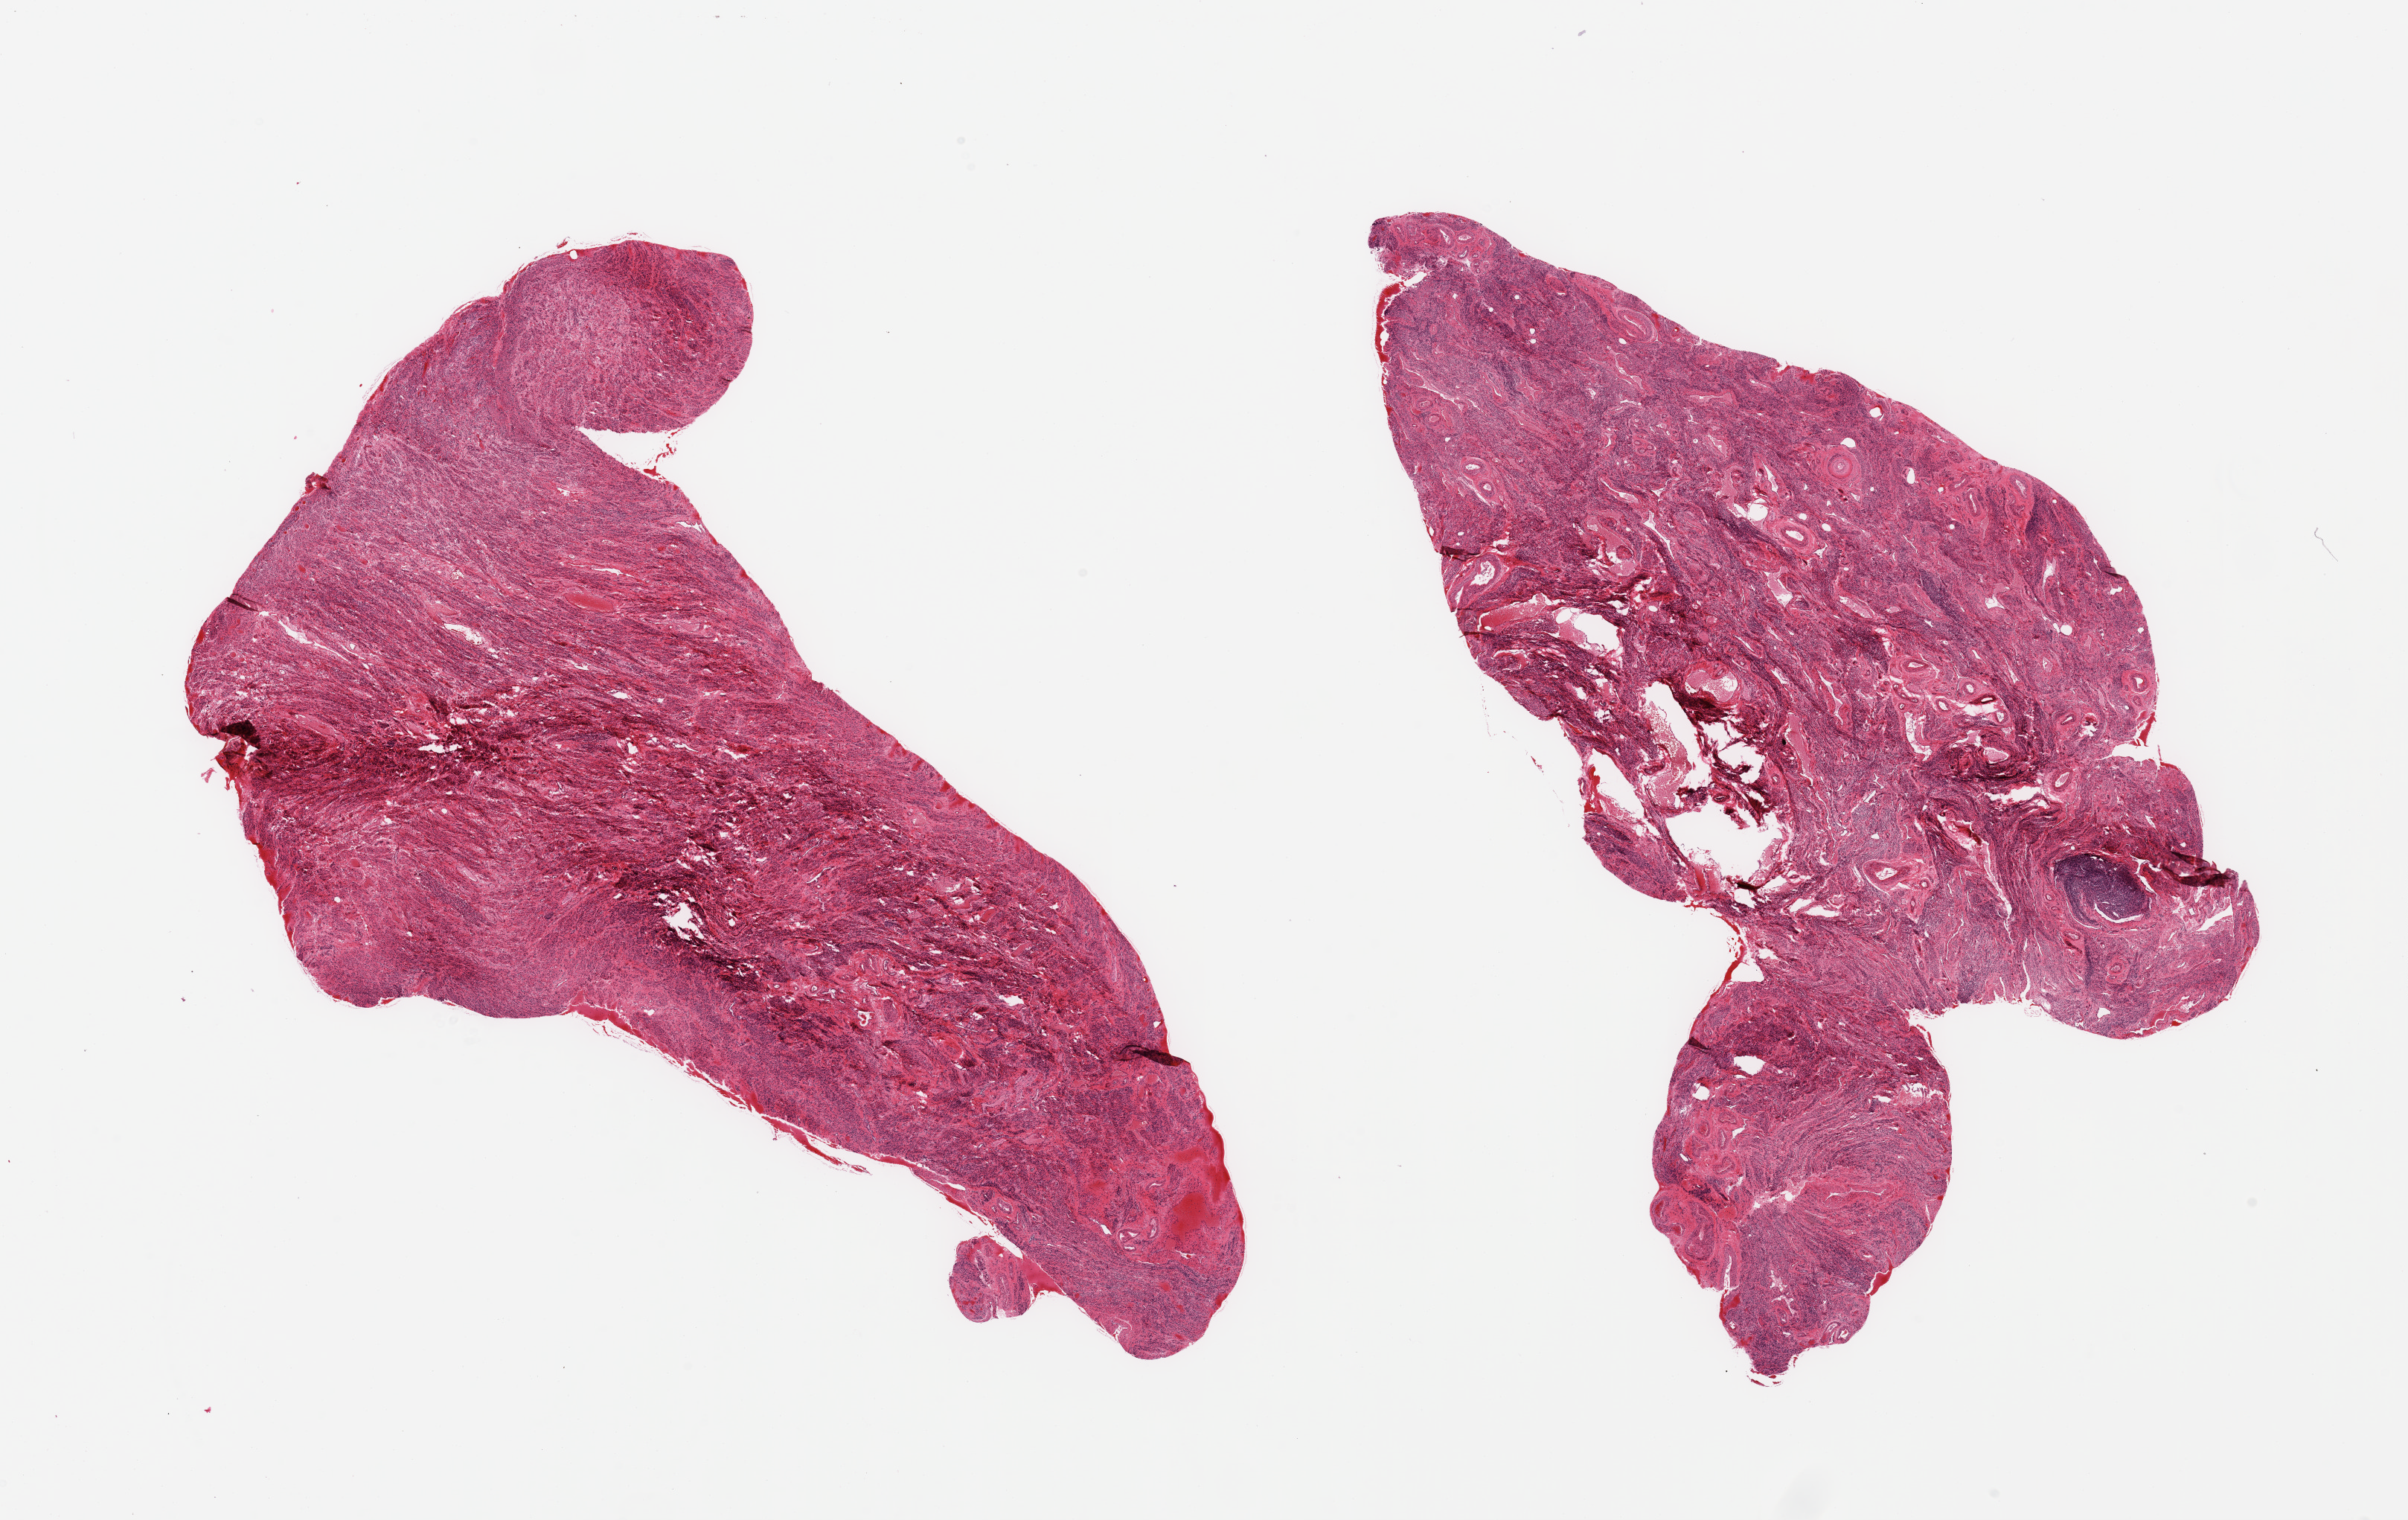
Hematoxylin and eosin (H&E) whole-slide image, brightfield, whole scanned area (about 25.6 x 16.2 mm) shown as a low-resolution overview; PAXgene-fixed, paraffin-embedded tissue; target tissue: uterus; tissue donor sample. Donor sex: female.
* review note (as recorded): 2 pieces